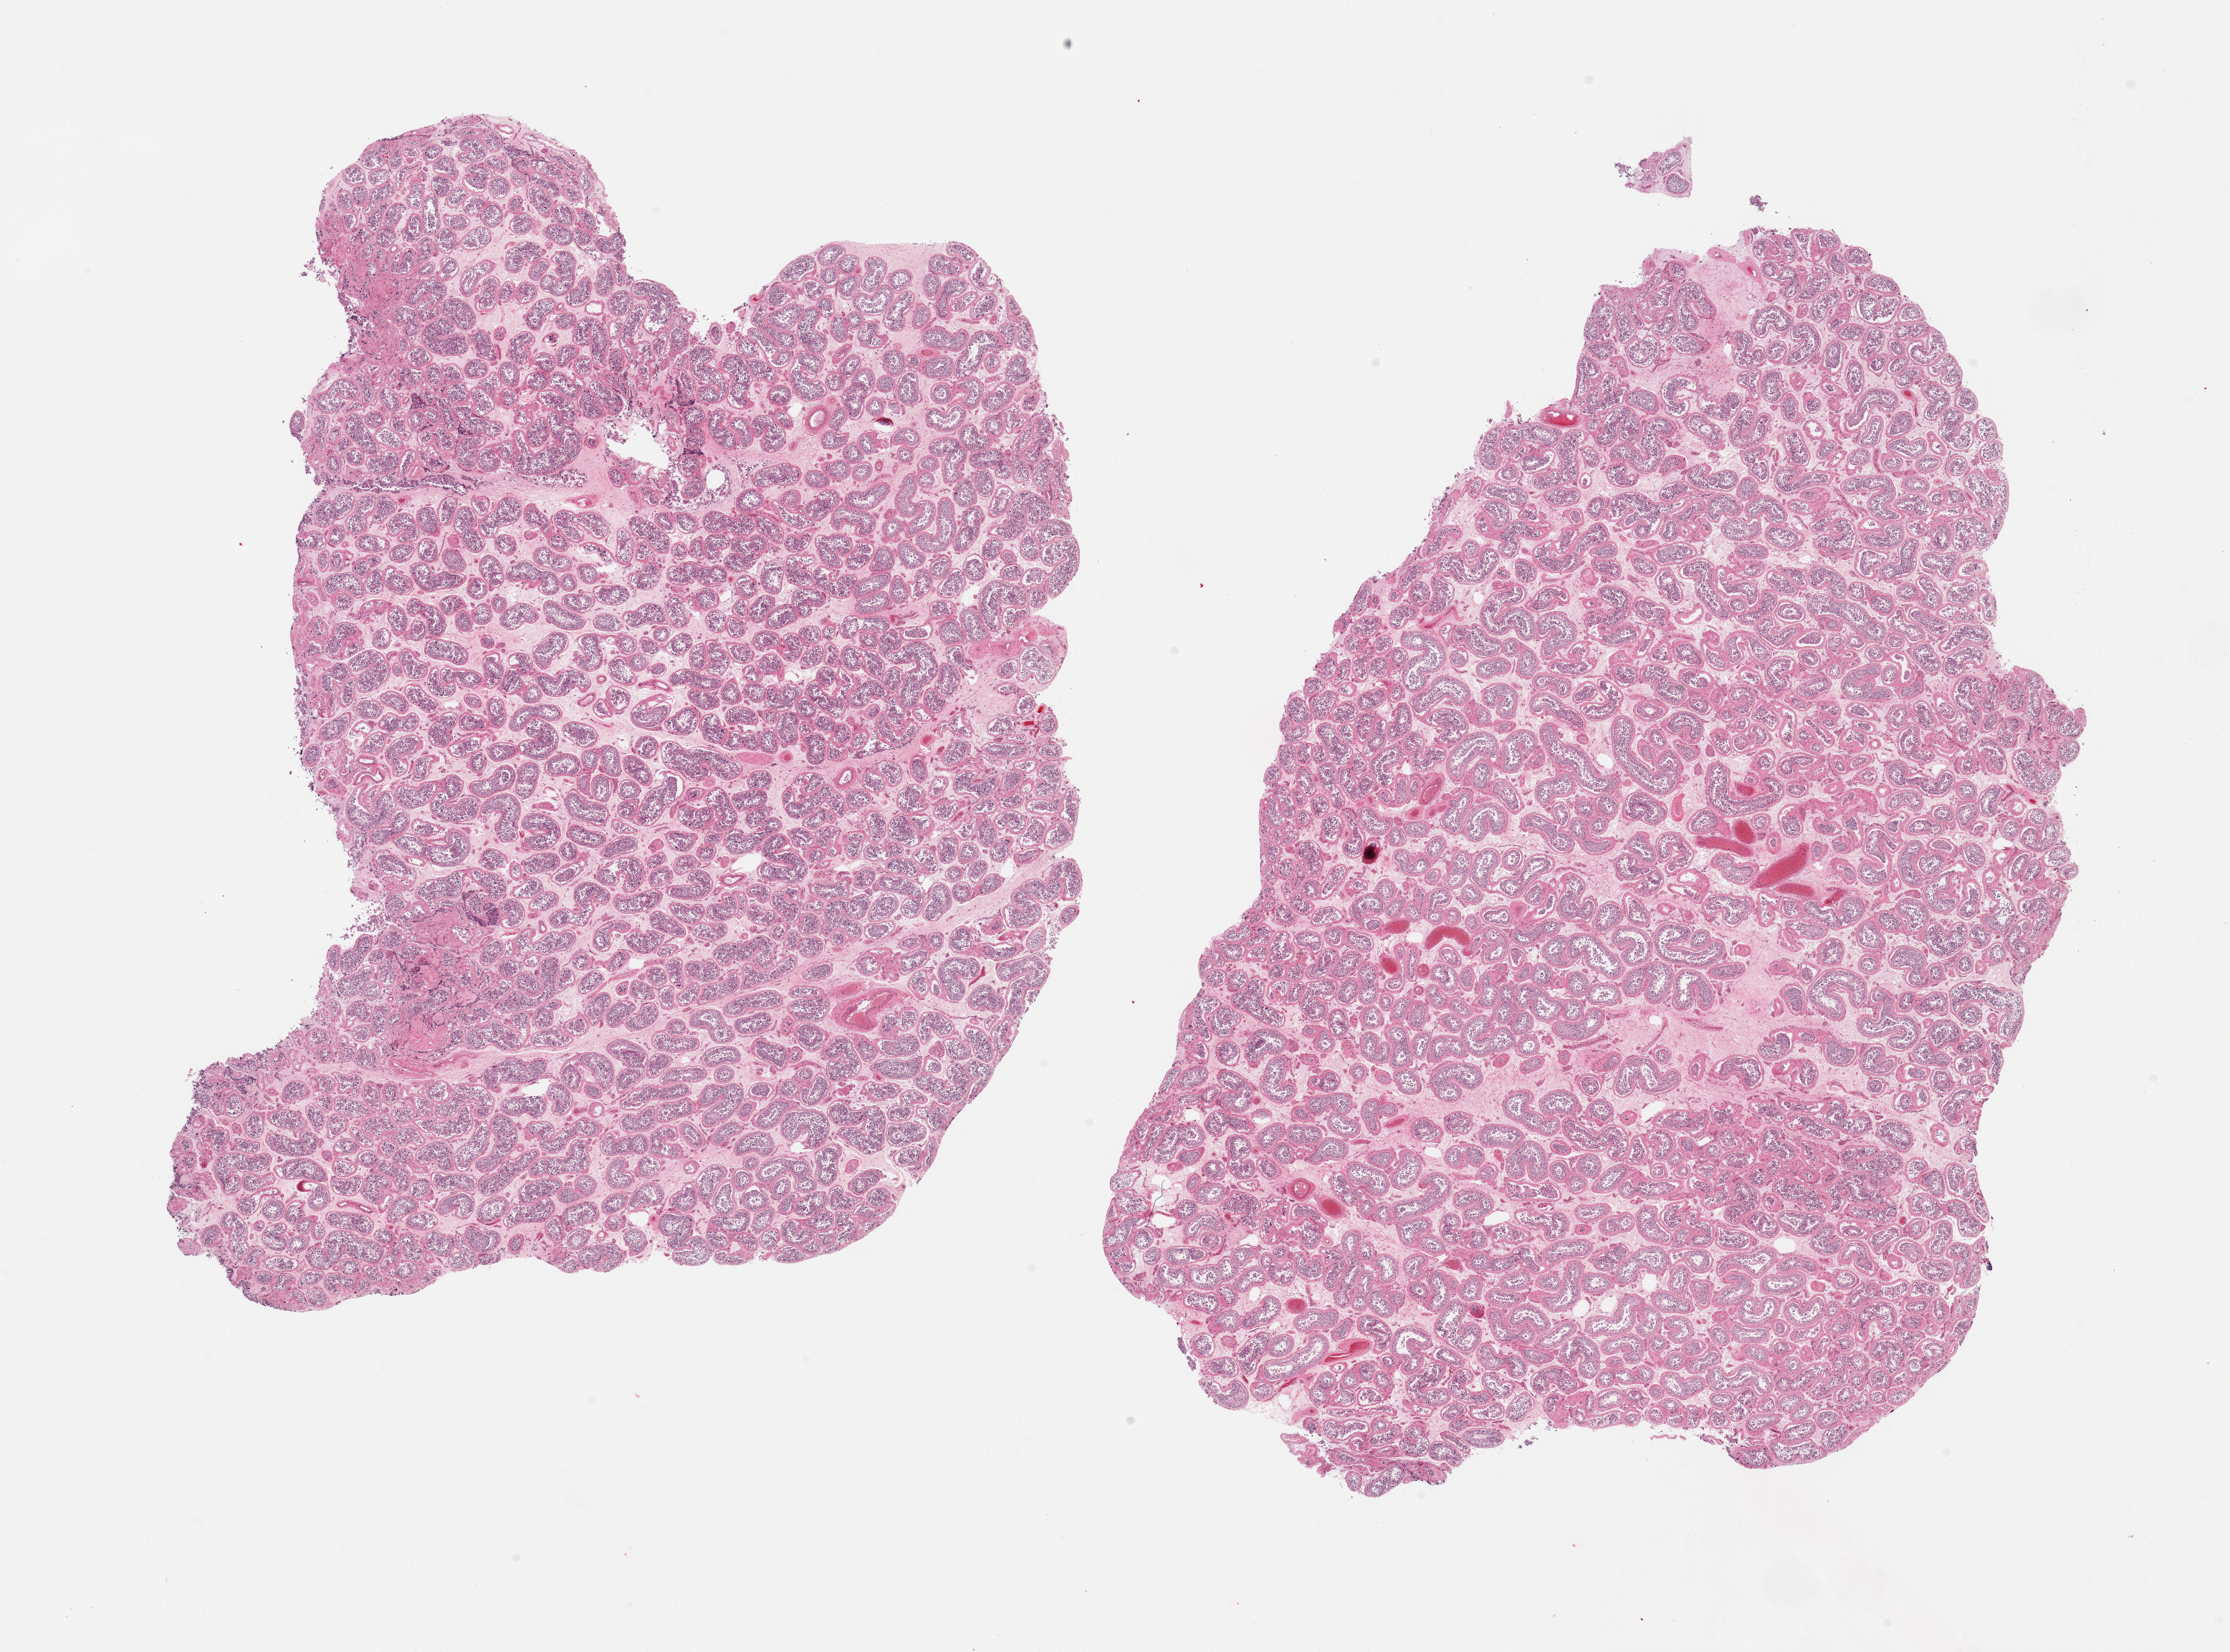
Hematoxylin and eosin (H&E) whole-slide image, brightfield, shown as a low-resolution overview of the whole scanned area (about 24.6 x 18.2 mm). PAXgene-fixed paraffin-embedded (PFPE) section. Sampled site (target tissue): testis. Donor tissue sample.
Reviewer comment on this tissue sample: 2 pieces, spermatogenesis appears present, assessment hampered by autolysis.